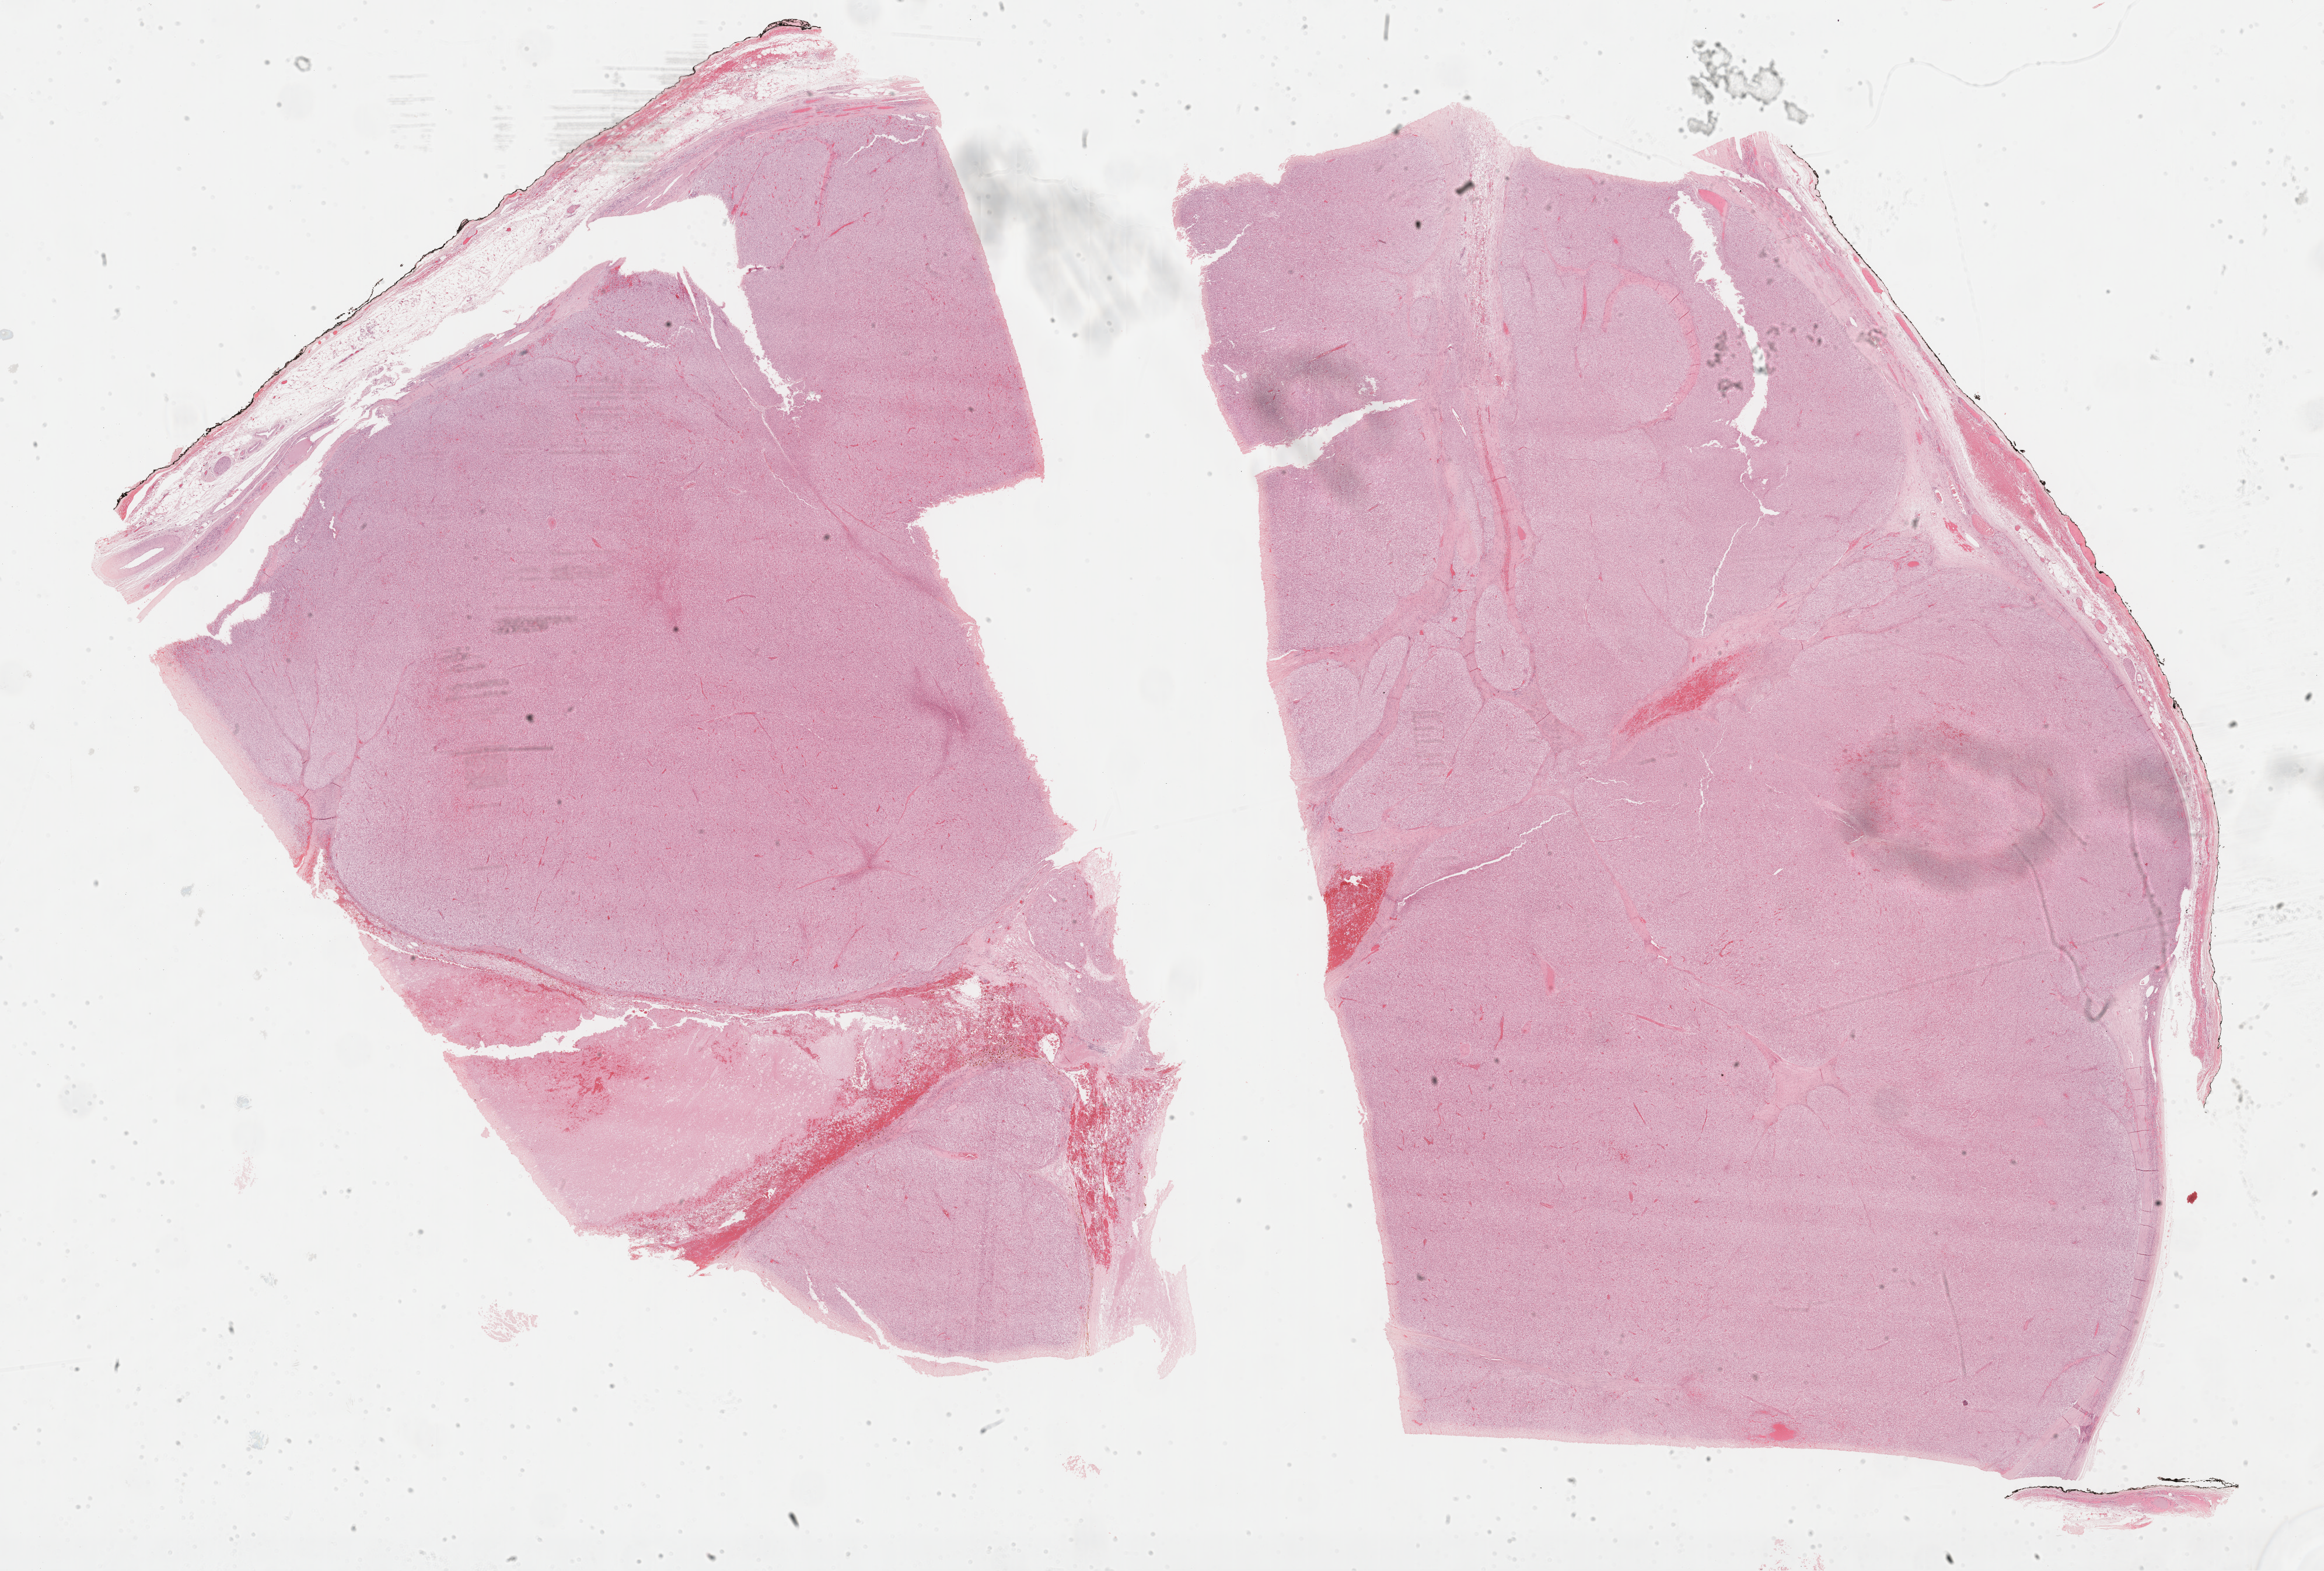
H&E-stained whole-slide image, whole scanned area (about 32.2 x 21.8 mm) shown as a low-resolution overview; formalin-fixed paraffin-embedded (FFPE) diagnostic section; primary tumour sample from the adrenal cortex. Male, age 48 years at initial diagnosis.
Laterality: left. Histologic diagnosis: Adrenal cortical carcinoma (cortex of adrenal gland).